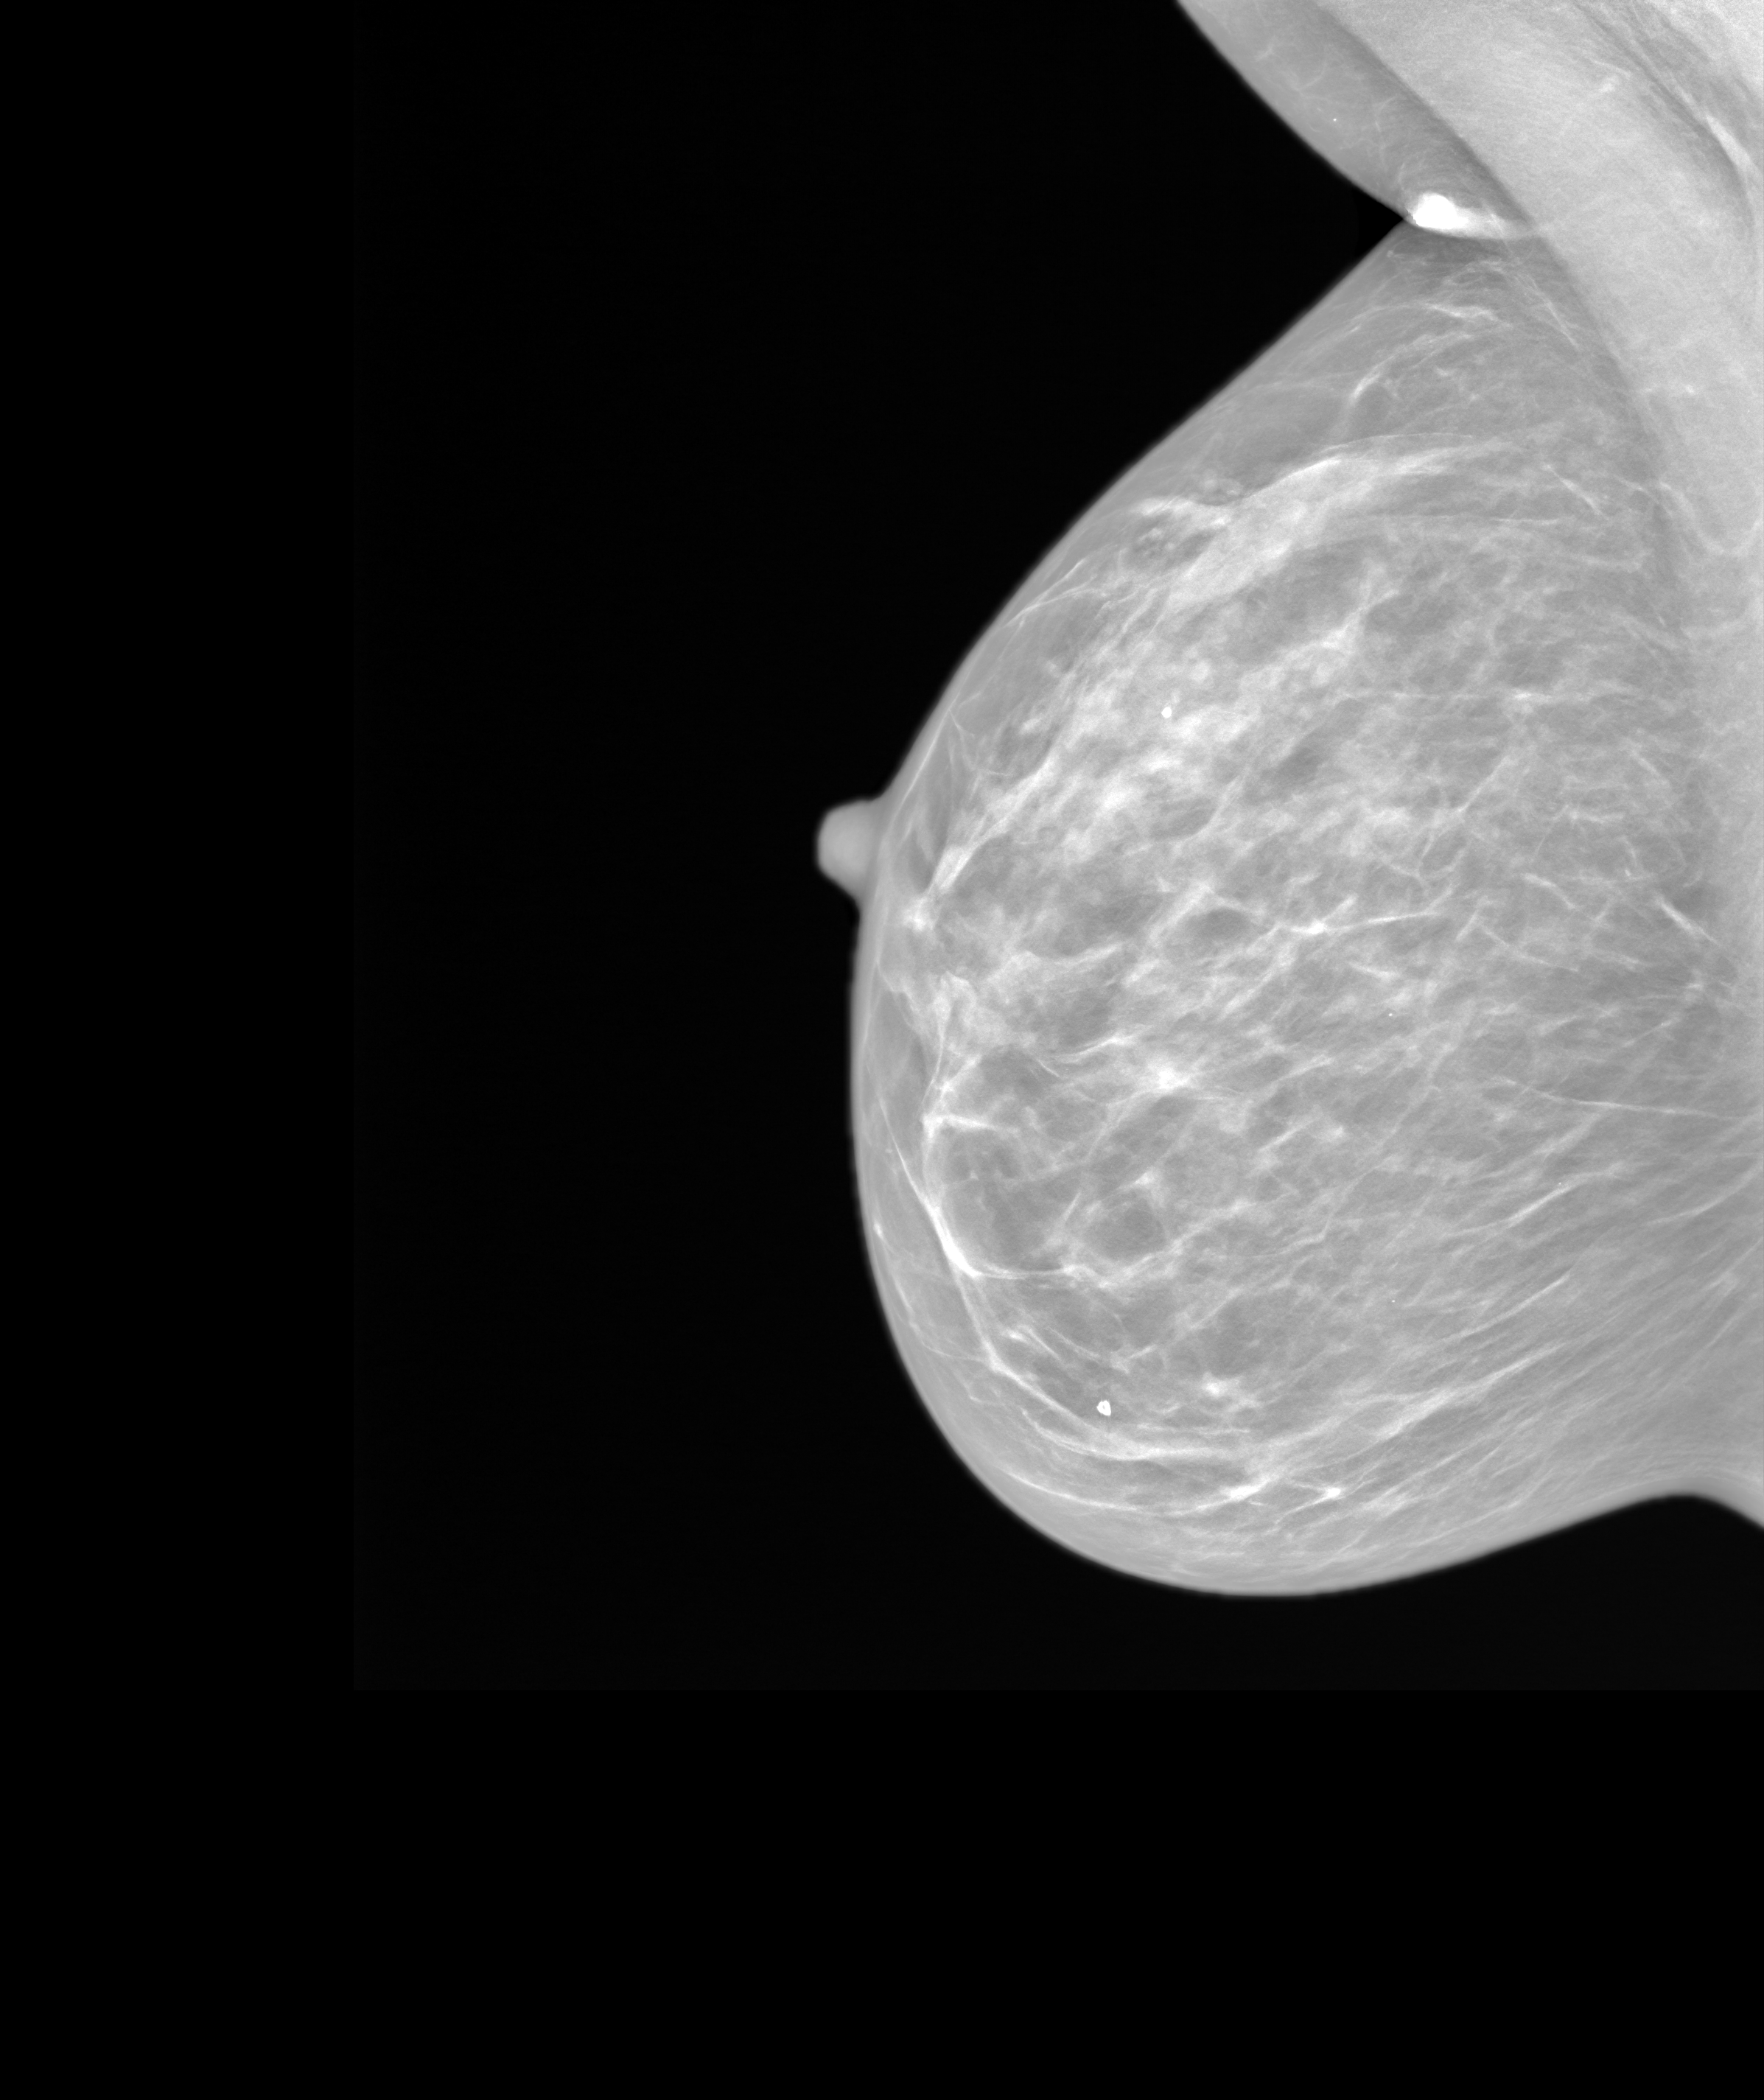
Annual screening mammography examination; system: SenoIris_1SP1.1(421).
Image type: synthesized 2-D view from tomosynthesis. Breast: right. Projection: mediolateral oblique (MLO) view.